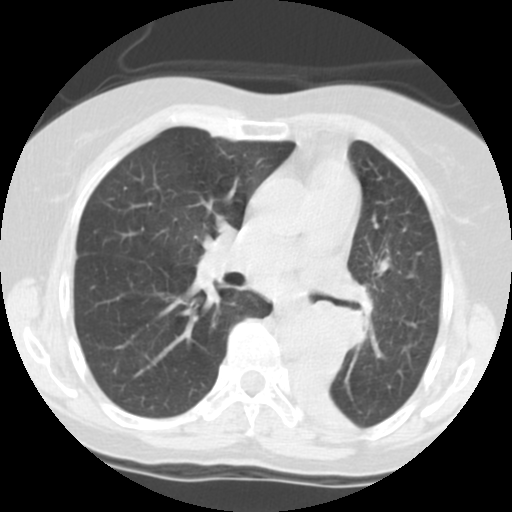
Low-dose screening chest CT, one axial slice; position 70 of 113 along the scan axis; lung window (W 1500 / L -600 HU); 512 × 512 image matrix, field of view 280 × 280 mm.
Outlined on this slice (expert manual segmentation):
- lesion 1 (tumor, left main bronchus): bounding box <302,302,363,367> (left, top, right, bottom; pixels)